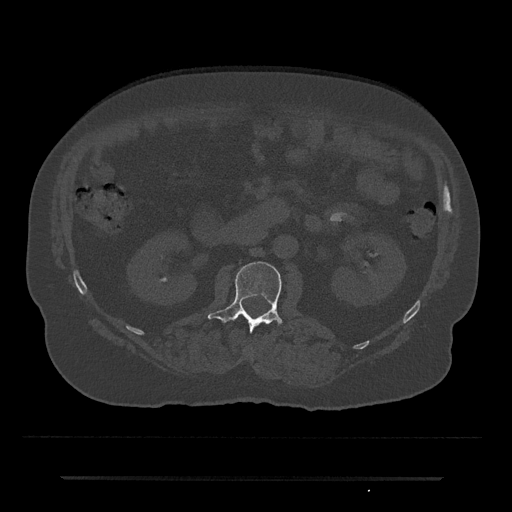
CT including the spine, one axial slice. Slice 16 of 797 in the series (ordered by position). 120 kVp. Bone window (W 1800 / L 400 HU). 512 × 512 image matrix, field of view 437 × 437 mm. Patient: male, 69 years. Case-level facts recorded for this patient, not image findings: primary cancer: prostate.
Structures marked on this image (semi-automatic segmentation, software-assisted and operator-edited):
- L2 vertebra: bounding box (x1, y1, x2, y2) in pixels: (208, 261, 283, 332)